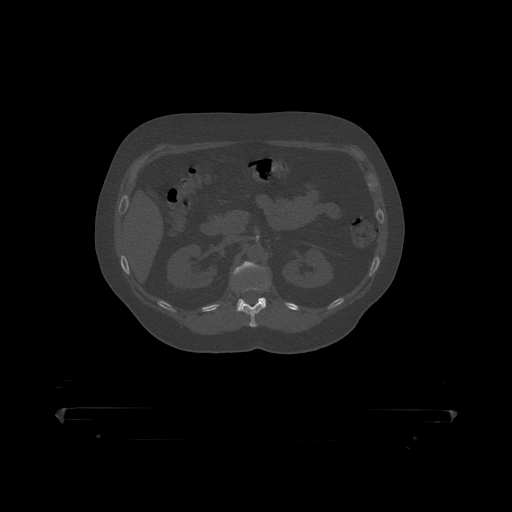
CT including the spine, one axial slice. Slice 159 of 390 in the series (ordered by position). Bone window (W 1800 / L 400 HU). 1.25 mm slice thickness. 512 × 512 image matrix, field of view 650 × 650 mm. Patient: male, 60 years. From the clinical record (not read from this slice): primary cancer: prostate.
Annotated regions visible in this slice (semi-automatic segmentation, software-assisted and operator-edited):
- L1 vertebra: bounding box <233,262,269,314> (left, top, right, bottom; pixels)
- T12 vertebra: <234,280,271,319>